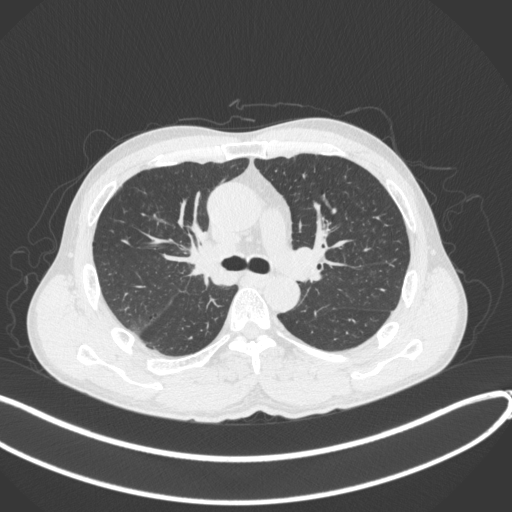
Chest CT, one axial slice; position 245 of 409 along the scan axis; reconstruction kernel B31f; 120 kVp; lung window (W 1500 / L -600 HU); 512 × 512 image matrix. Patient: male, 53 years. From the clinical record (not read from this slice): clinical TNM (as recorded): T1b N0 M0.
Structures marked on this image (rectangle marked by the reading radiologist):
- lung tumour (recorded histology: squamous cell carcinoma): bounding box <181,236,238,291> (left, top, right, bottom; pixels)